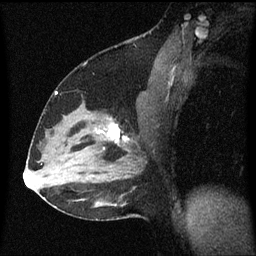
Breast MRI (dynamic contrast-enhanced), one sagittal slice. Position 37 of 60 along the scan axis. Dynamic contrast-enhanced series, image 2 of 3 at this slice position (ordered by acquisition). 1.5 T. TE 4.2 ms, TR 8.4 ms. 2 mm slice thickness. 256 × 256 image matrix, field of view 200 × 200 mm. Patient: female, 37 years. From the clinical record (not read from this slice): setting: breast cancer imaged before/during neoadjuvant chemotherapy; receptor status: HR-positive, HER2-negative.
Annotated regions visible in this slice (semi-automatically segmented with operator editing):
- analysis volume of interest (the breast-tissue region the enhancement analysis was run in; not a lesion): box from (x=94, y=112) to (x=137, y=157) px
- tumour enhancement mask (voxels above the 70 % enhancement threshold inside the analysis volume of interest): (x=99, y=124)–(x=126, y=143)